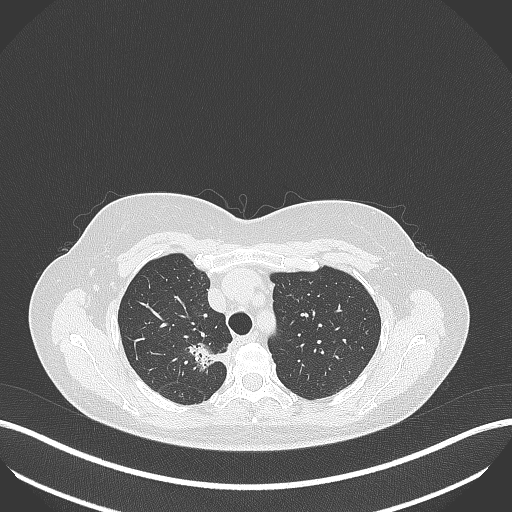
Chest CT, one axial slice; position 303 of 386 along the scan axis; 120 kVp; lung window (W 1500 / L -600 HU); 1 mm slice thickness; 512 × 512 image matrix, field of view 400 × 400 mm. Female patient, age 65 years. Case-level facts recorded for this patient, not image findings: clinical TNM (as recorded): T1b N0 M0; histopathological grade: G2.
Annotated regions visible in this slice (bounding box drawn by a radiologist):
- lung tumour (recorded histology: adenocarcinoma): box from (x=187, y=334) to (x=230, y=375) px